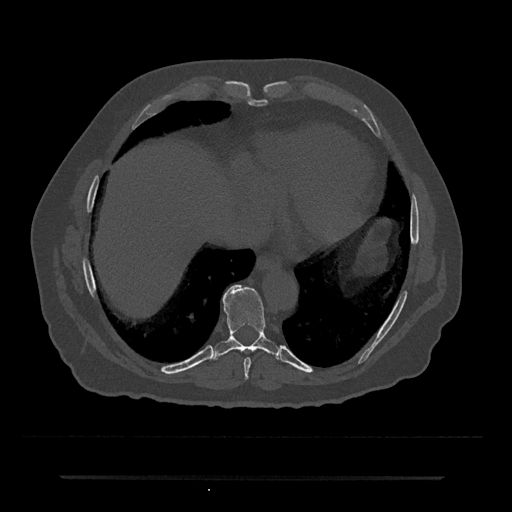
CT including the spine, one axial slice; reconstruction kernel Br40s/3; bone window (W 1800 / L 400 HU); 512 × 512 image matrix, field of view 437 × 437 mm. Male patient, age 69 years. Case-level facts recorded for this patient, not image findings: primary cancer: prostate.
Annotated regions visible in this slice (semi-automatic segmentation, software-assisted and operator-edited):
- T8 vertebra: box from (x=244, y=358) to (x=251, y=379) px
- T9 vertebra: (x=213, y=285)–(x=281, y=360)